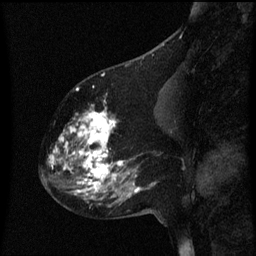
Breast MRI (dynamic contrast-enhanced), one sagittal slice; slice 27 of 60 in the series (ordered by position); dynamic contrast-enhanced series, image 2 of 3 at this slice position (ordered by acquisition); 1.5 T; TE 4.2 ms, TR 8 ms; 2 mm slice thickness; 256 × 256 image matrix. Female patient, age 60 years.
Outlined on this slice (semi-automatic segmentation, software-assisted and operator-edited):
- analysis volume of interest (the breast-tissue region the enhancement analysis was run in; not a lesion): bounding box <49,108,158,197> (left, top, right, bottom; pixels)
- tumour enhancement mask (voxels above the 70 % enhancement threshold inside the analysis volume of interest): <50,110,141,197>